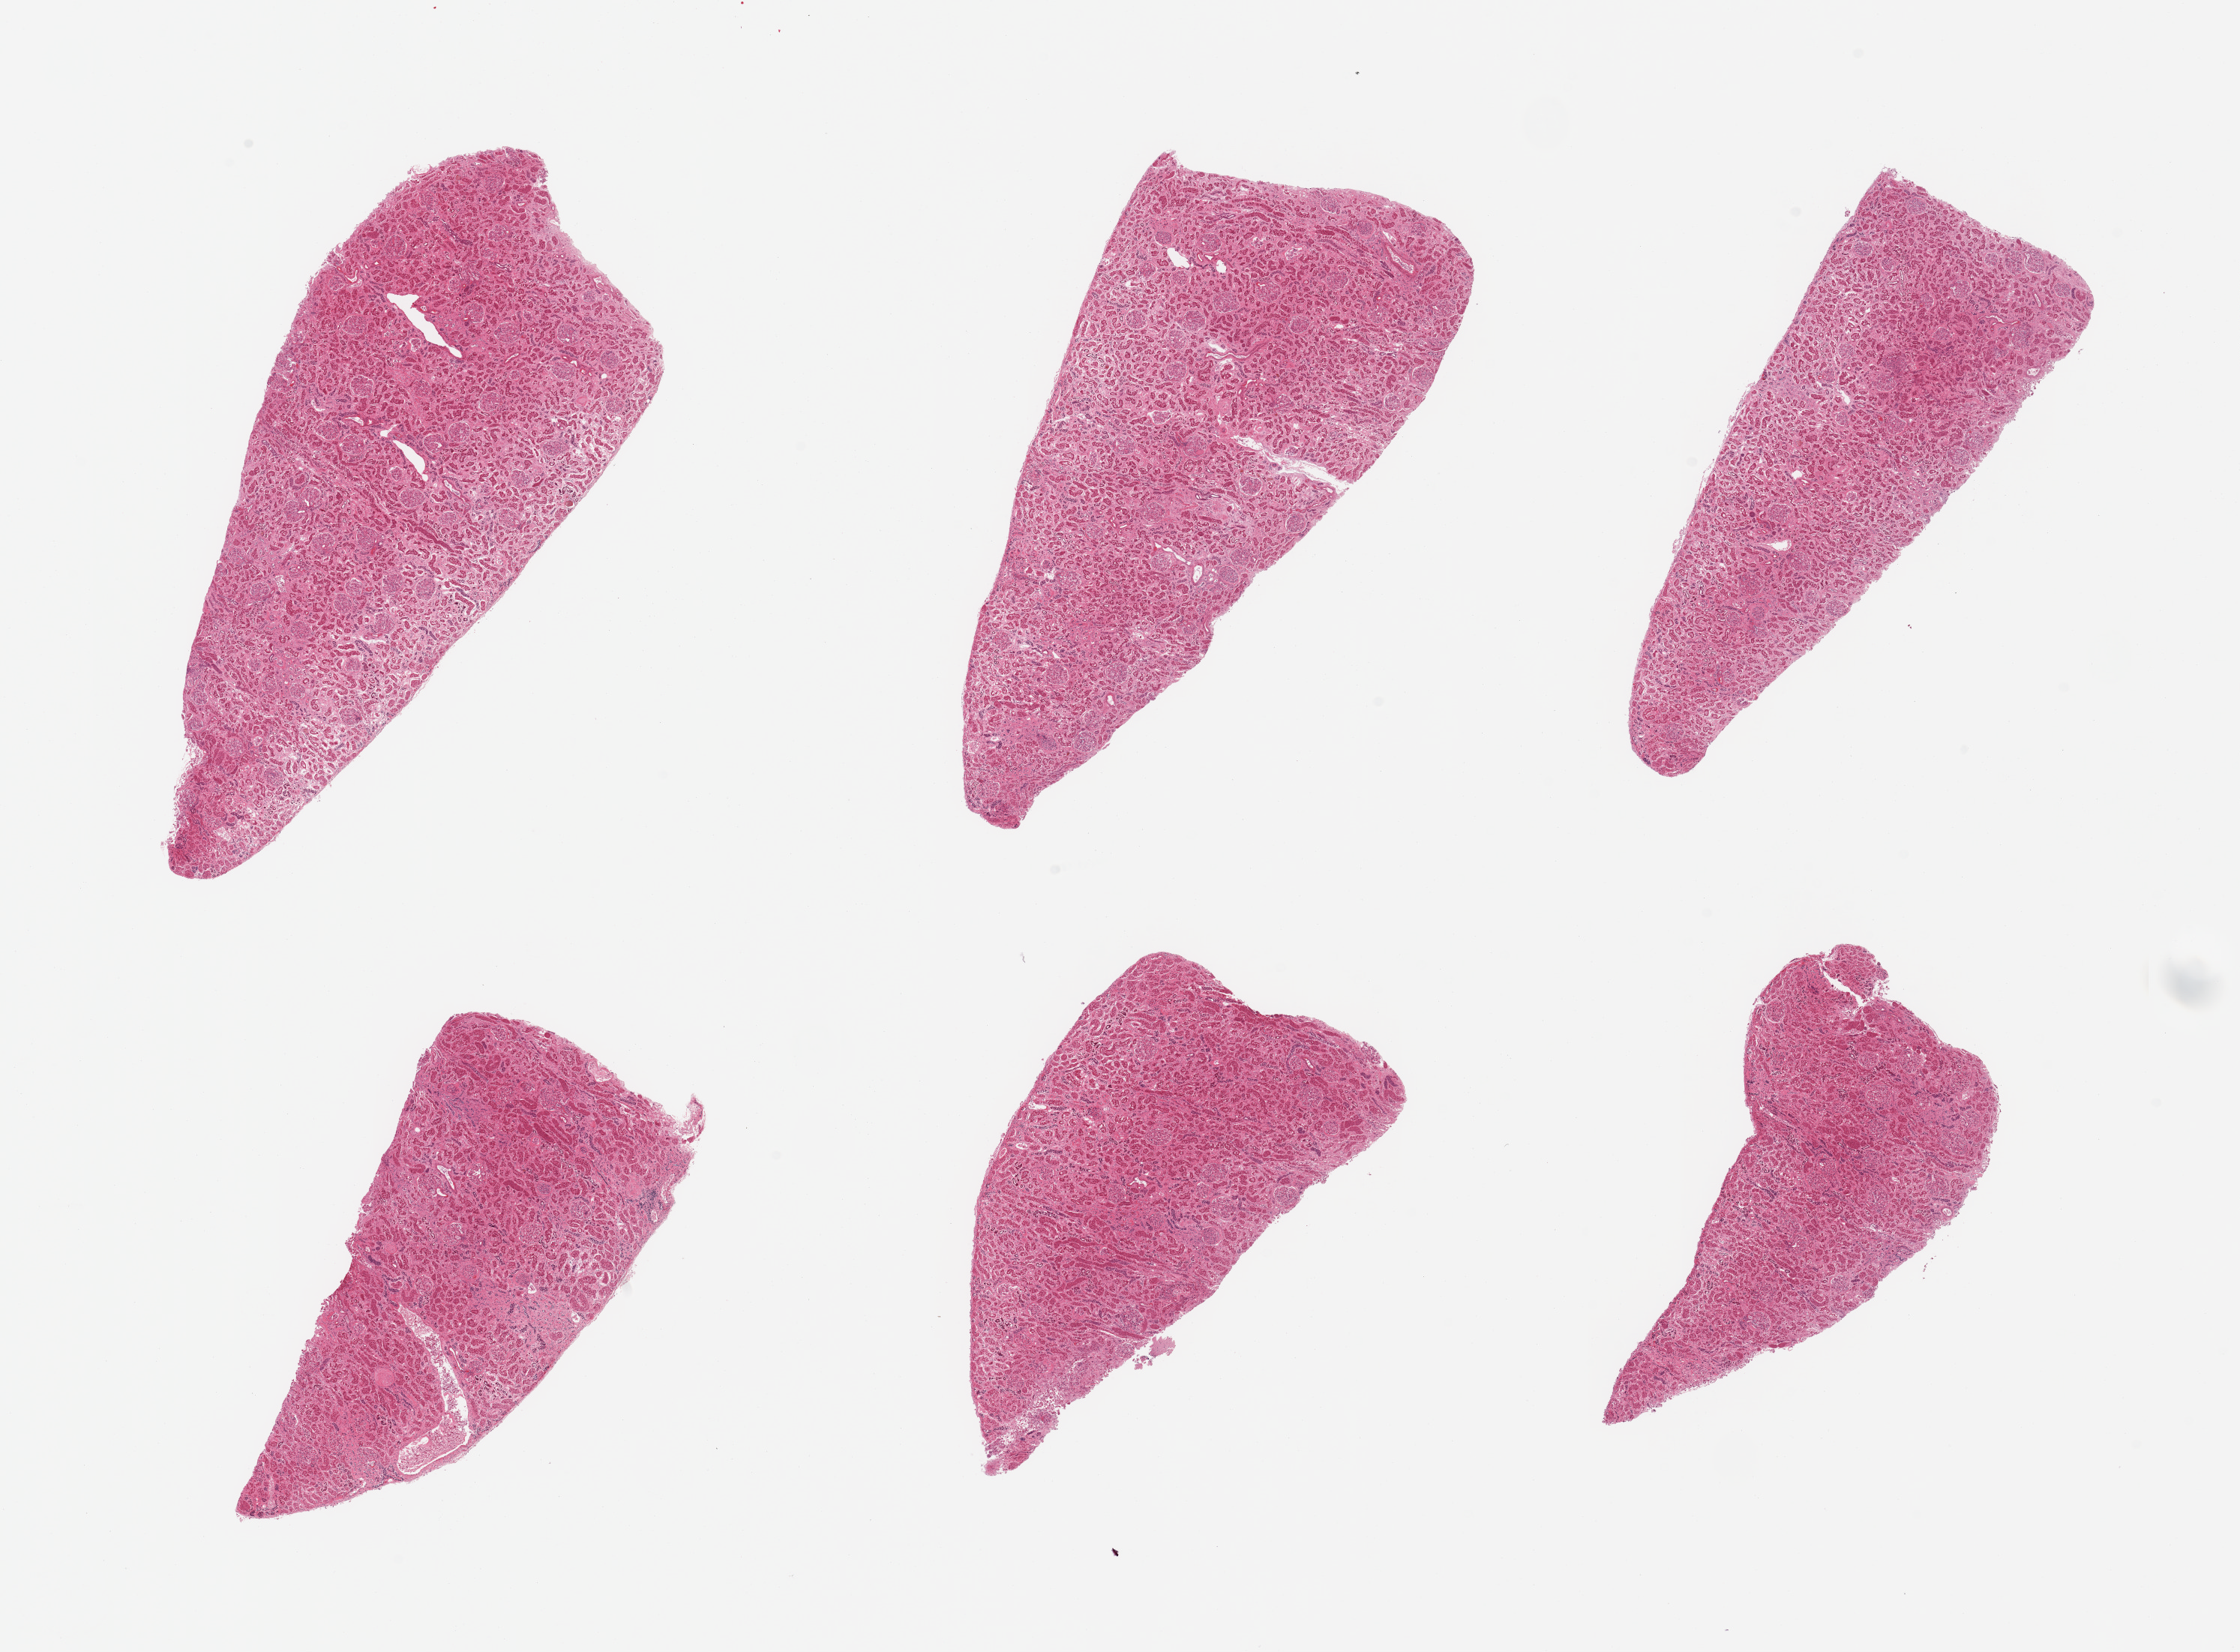
Digitized hematoxylin and eosin (H&E)-stained section — a low-resolution overview of the entire scanned area, about 23.6 x 17.4 mm. PAXgene-fixed, paraffin-embedded tissue. Target tissue: renal cortex. Donor tissue sample. Donor sex: female.
Pathologist's review note for this sample: 6 pieces; arteriolar and glomerular (nodular) sclerosis; tubules severely autolyzed.